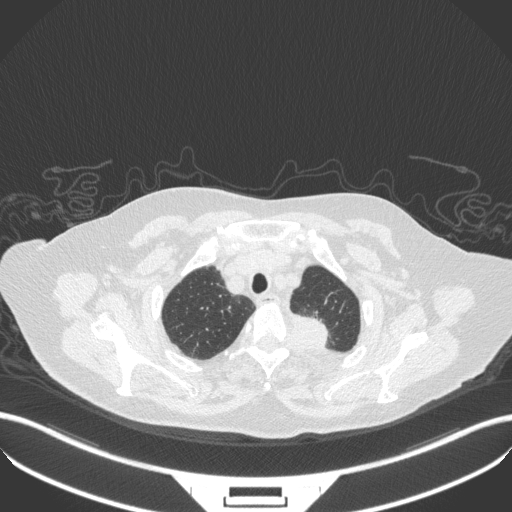
Chest CT, one axial slice; slice 300 of 353 in the series (ordered by position); lung window (W 1500 / L -600 HU); 1 mm slice thickness; 512 × 512 image matrix, field of view 400 × 400 mm. Patient: female, 81 years. Case-level facts recorded for this patient, not image findings: clinical TNM (as recorded): T2a N0 M0.
Structures marked on this image (bounding box drawn by a radiologist):
- lung tumour (recorded histology: adenocarcinoma): bounding box <285,306,335,354> (left, top, right, bottom; pixels)